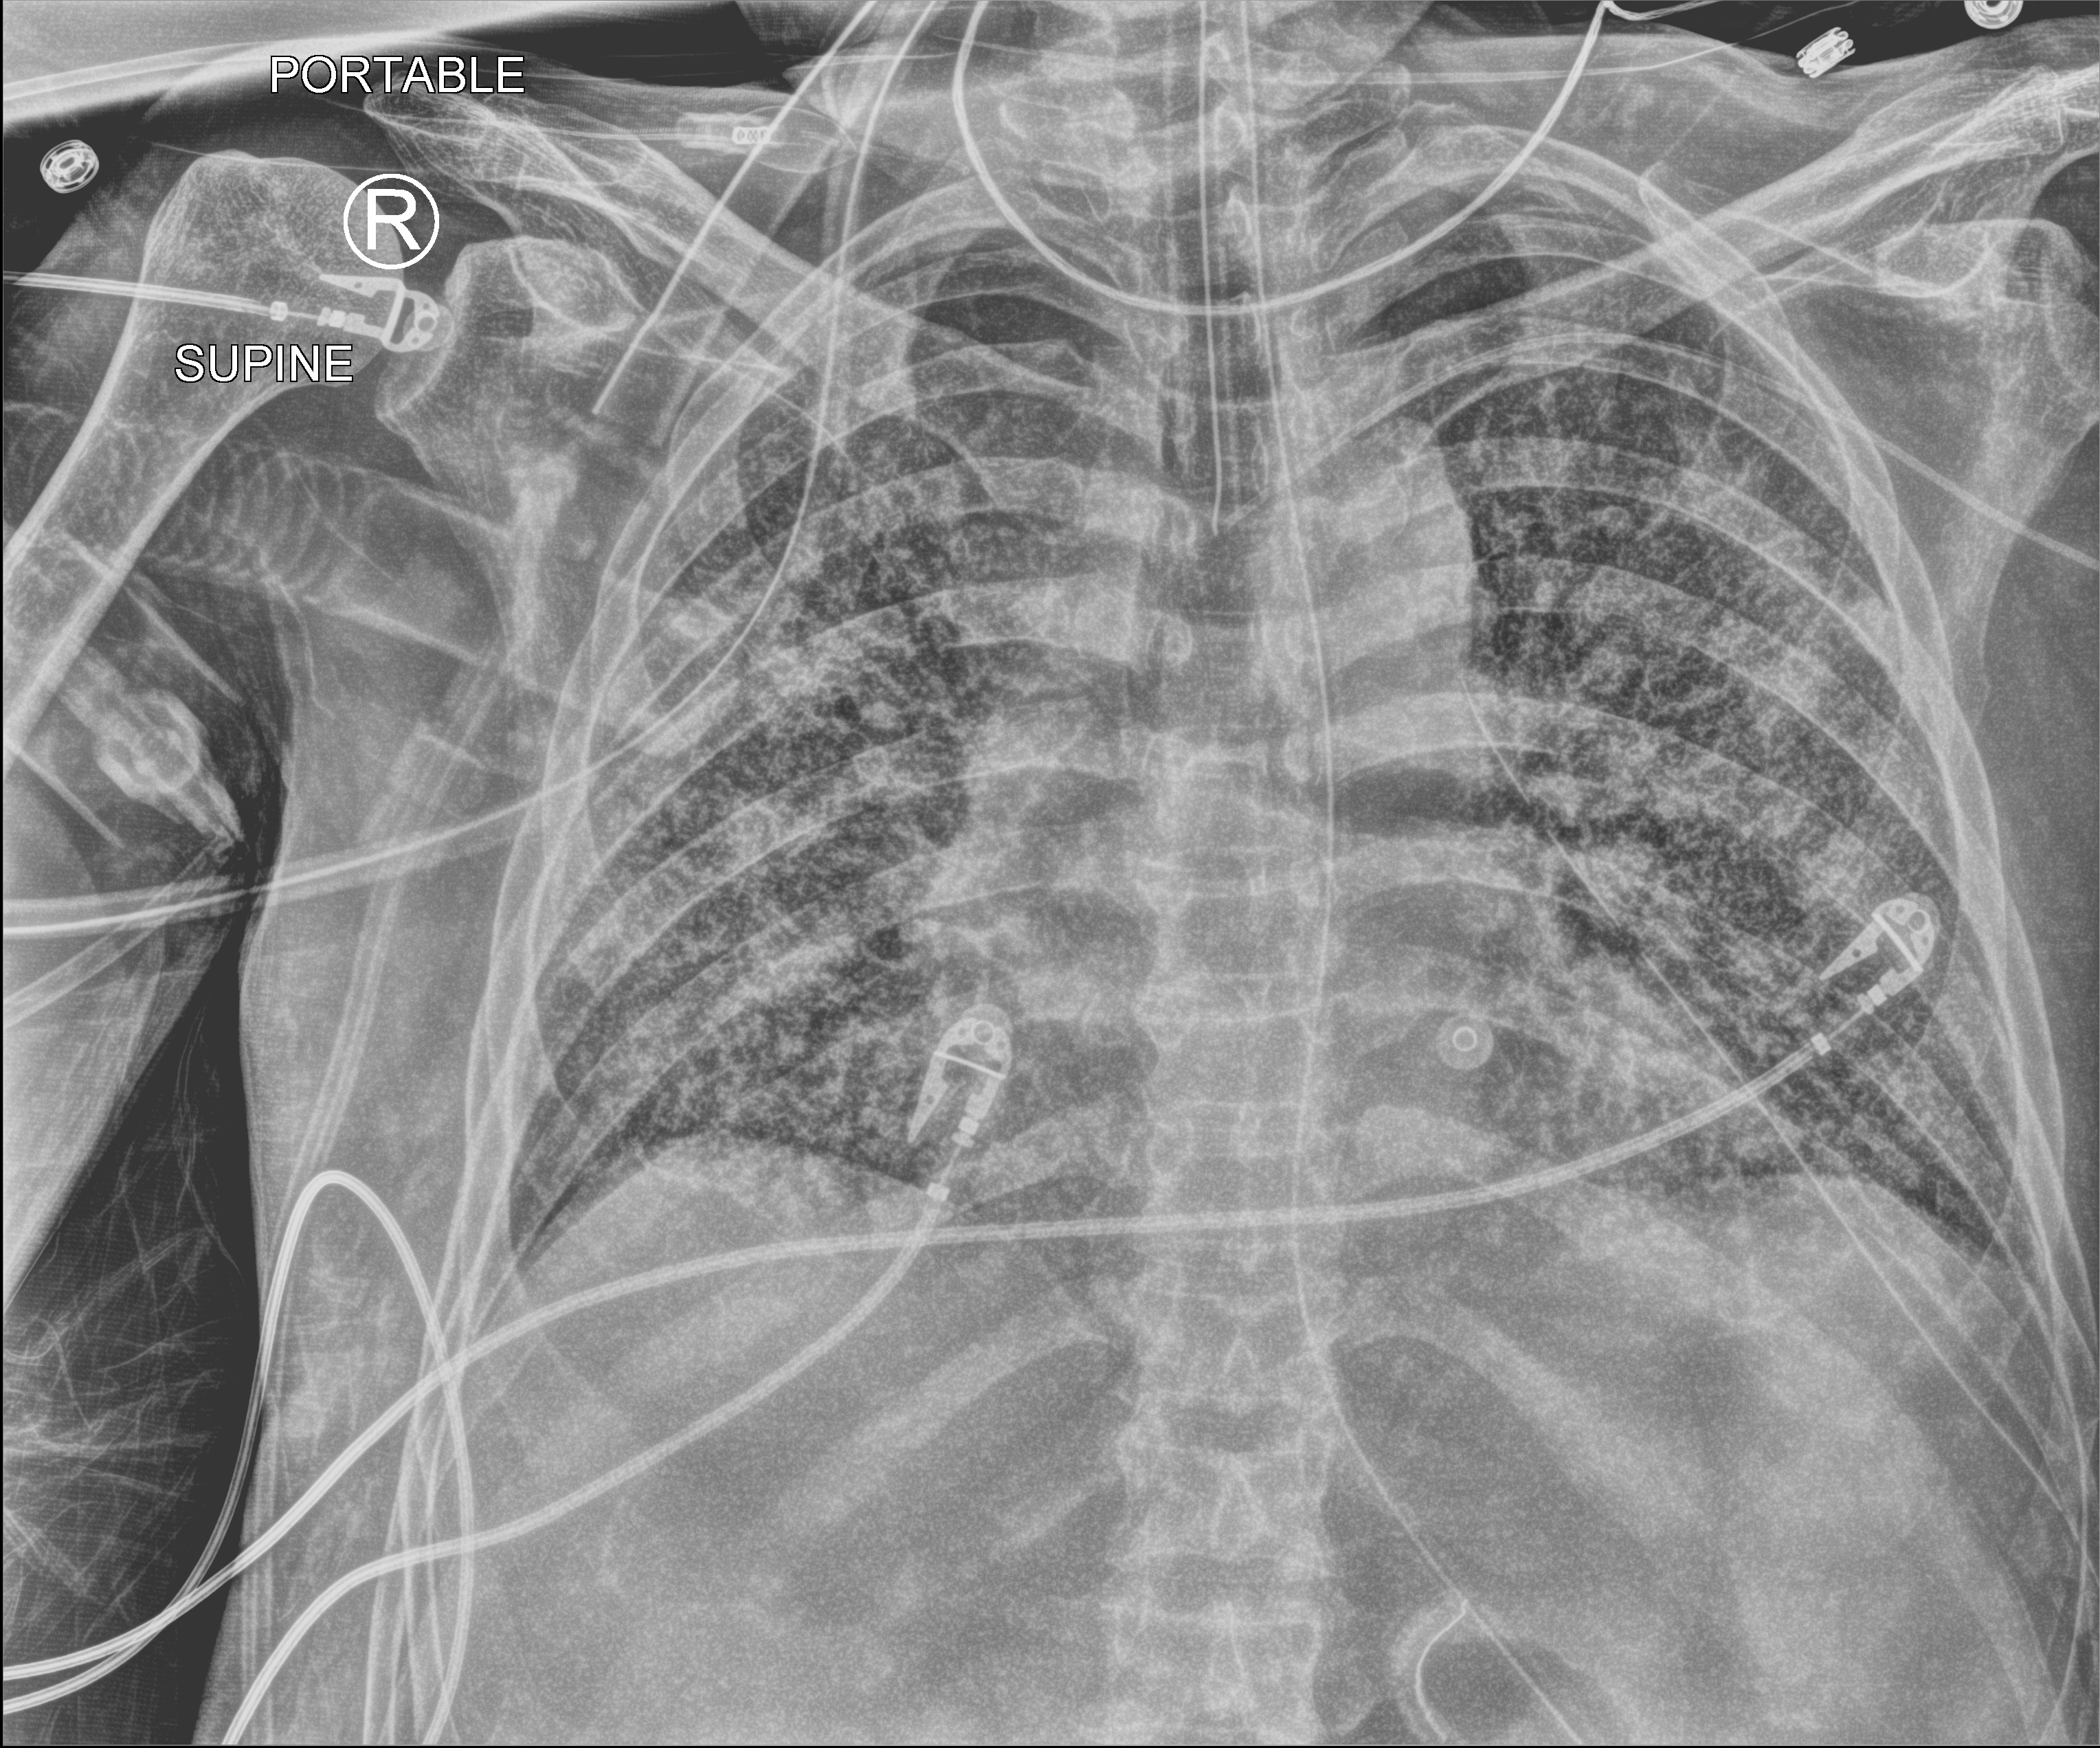
Portable chest radiograph; anteroposterior (AP) projection. Patient hospitalised with COVID-19; male, aged 60–74 years.
Admission-level facts for this patient (not findings on this image; timing relative to this image not recorded): mechanically ventilated during this hospital stay: yes.